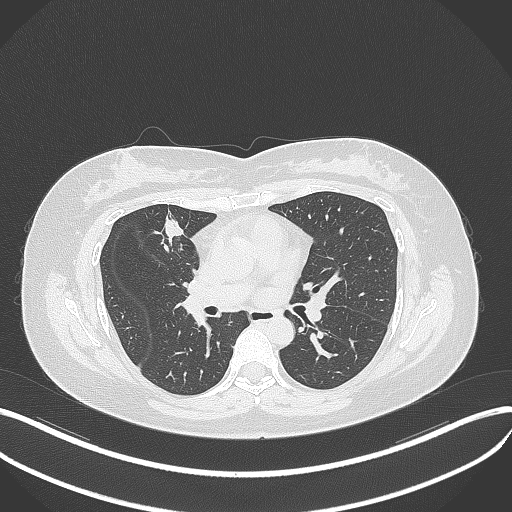
Chest CT, one axial slice. Position 172 of 273 along the scan axis. Lung window (W 1500 / L -600 HU). 1 mm slice thickness. 512 × 512 image matrix, field of view 400 × 400 mm. Female patient, age 42 years. Case-level facts recorded for this patient, not image findings: clinical TNM (as recorded): T1b N0 M0.
Outlined on this slice (rectangle marked by the reading radiologist):
- lung tumour (recorded histology: adenocarcinoma): bounding box <155,211,183,253> (left, top, right, bottom; pixels)